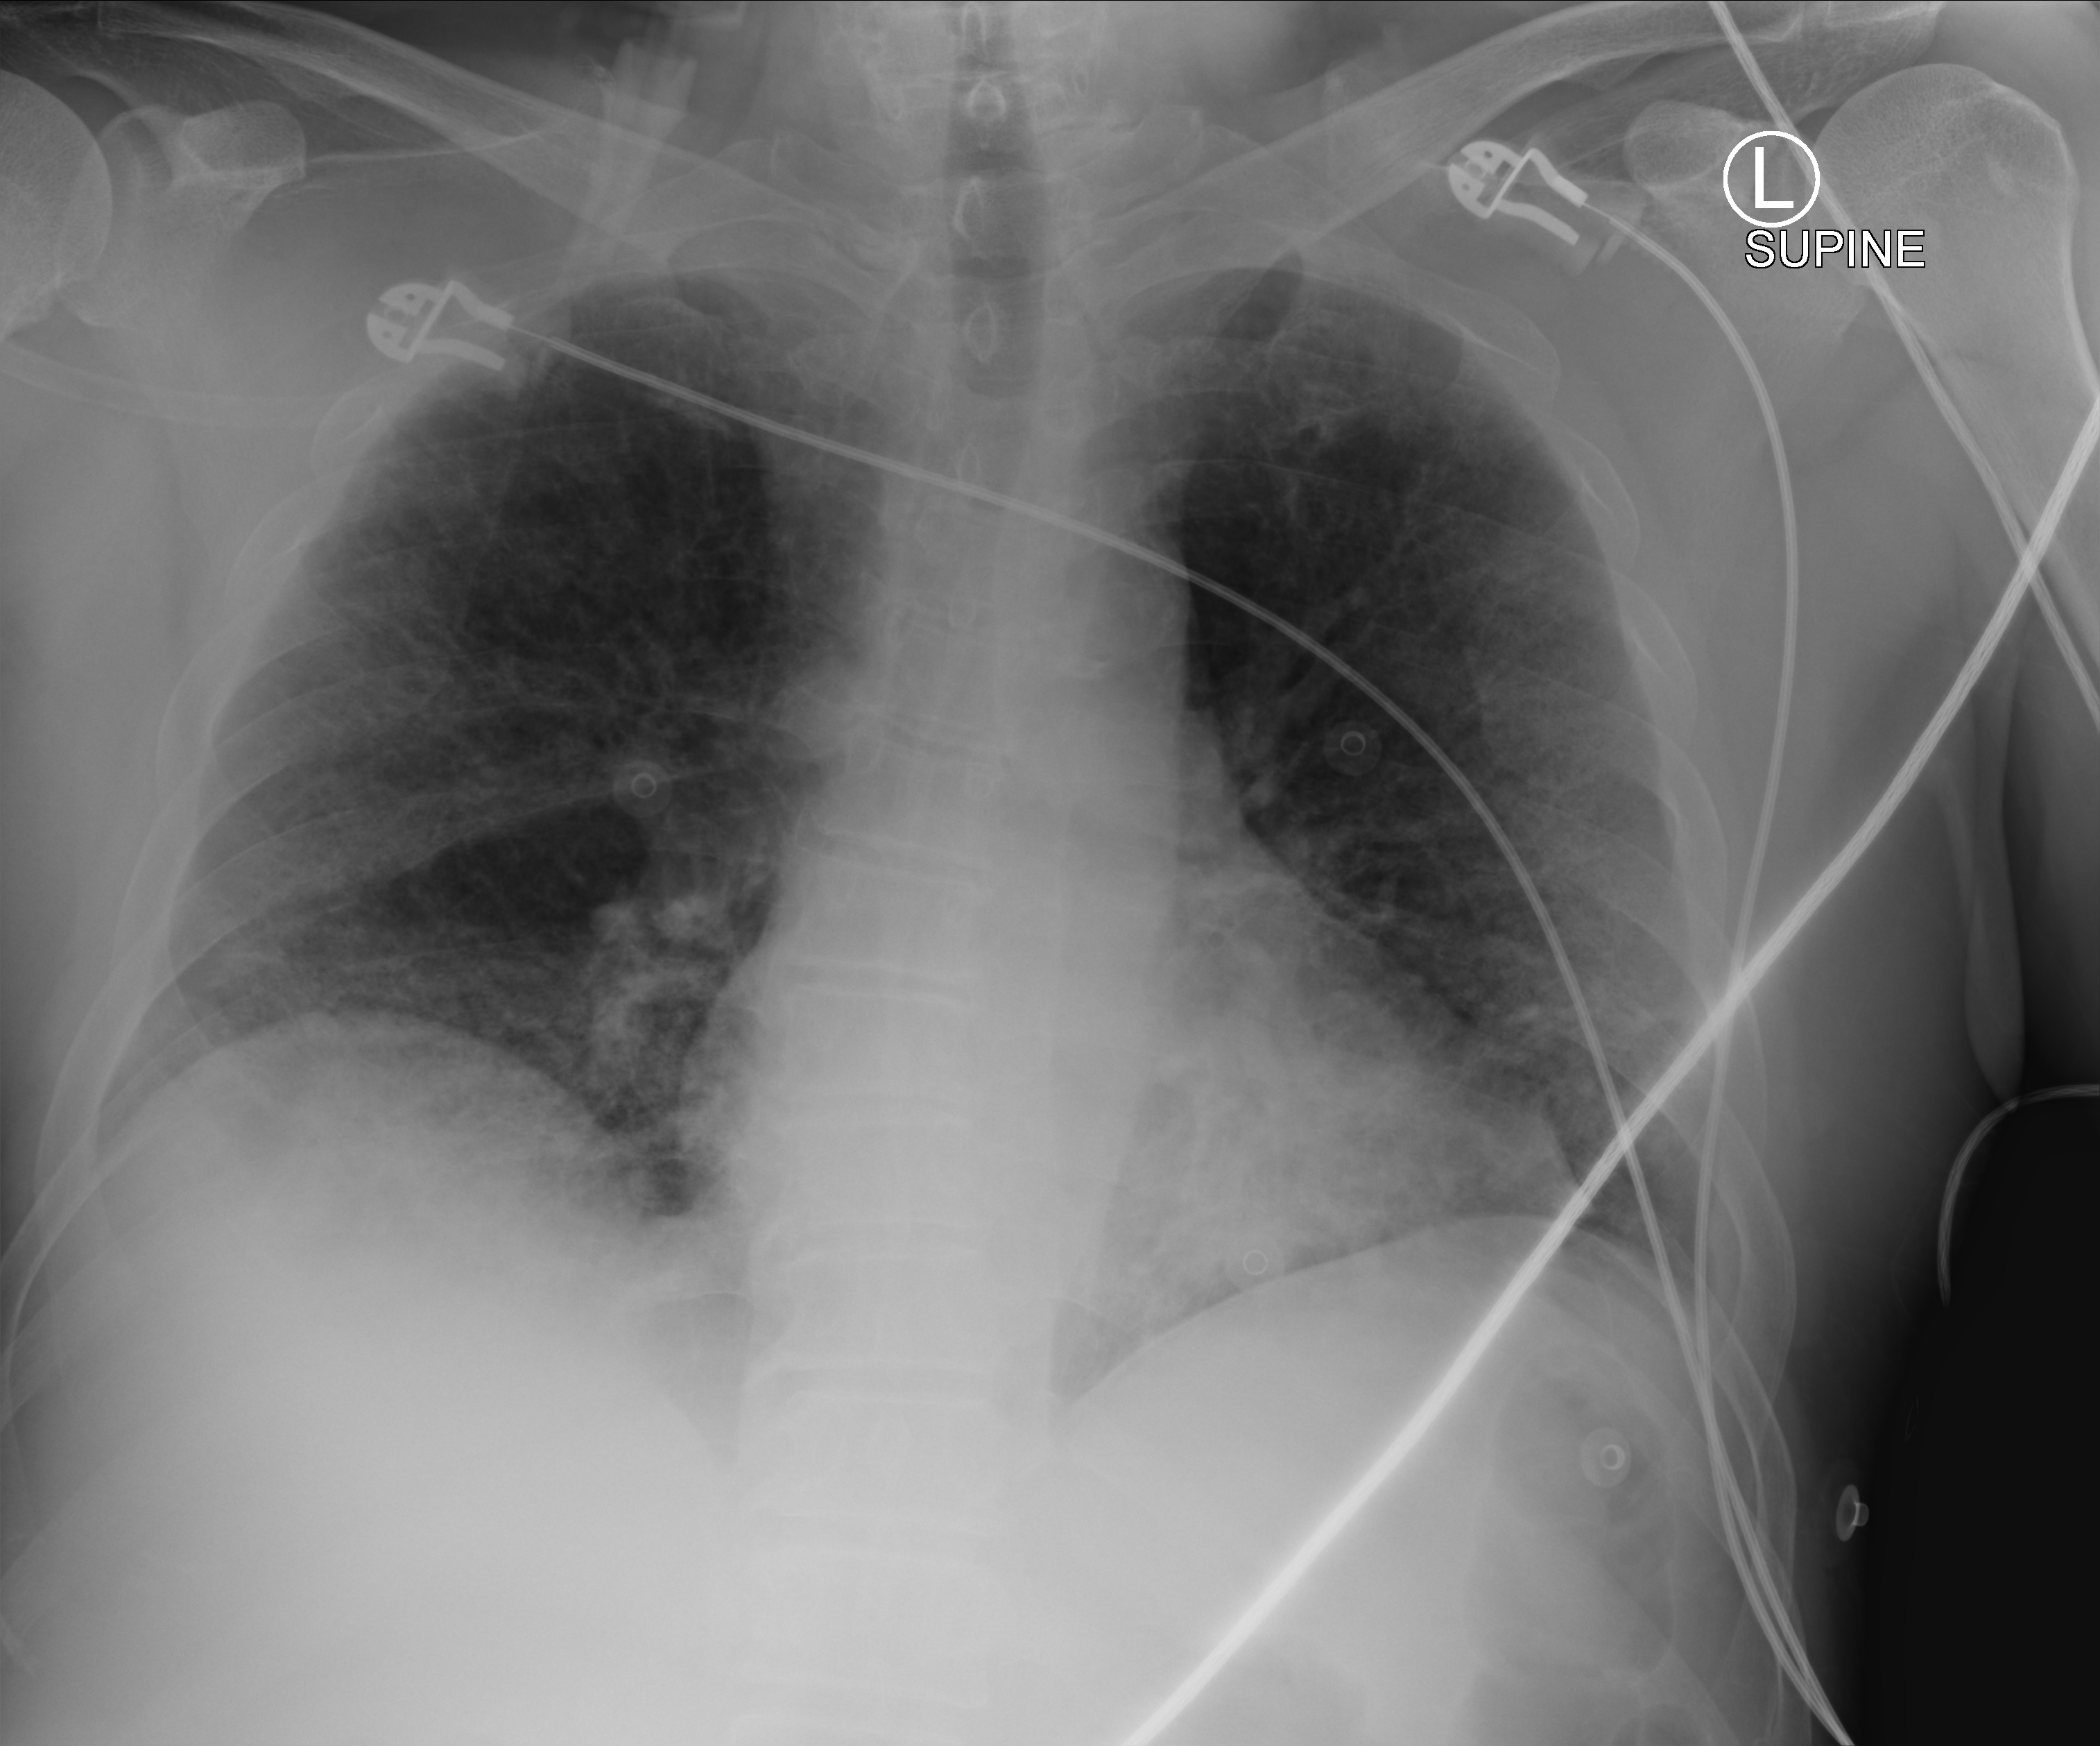
Bedside chest radiograph (computed radiography); anteroposterior (AP) projection. Patient hospitalised with COVID-19; male, aged 18–59 years.
From the hospital-stay record, not from the radiograph (when in the stay this image was taken is not recorded): mechanically ventilated during this hospital stay: no; COPD (admission record): no; admitted to intensive care during this hospital stay: no.